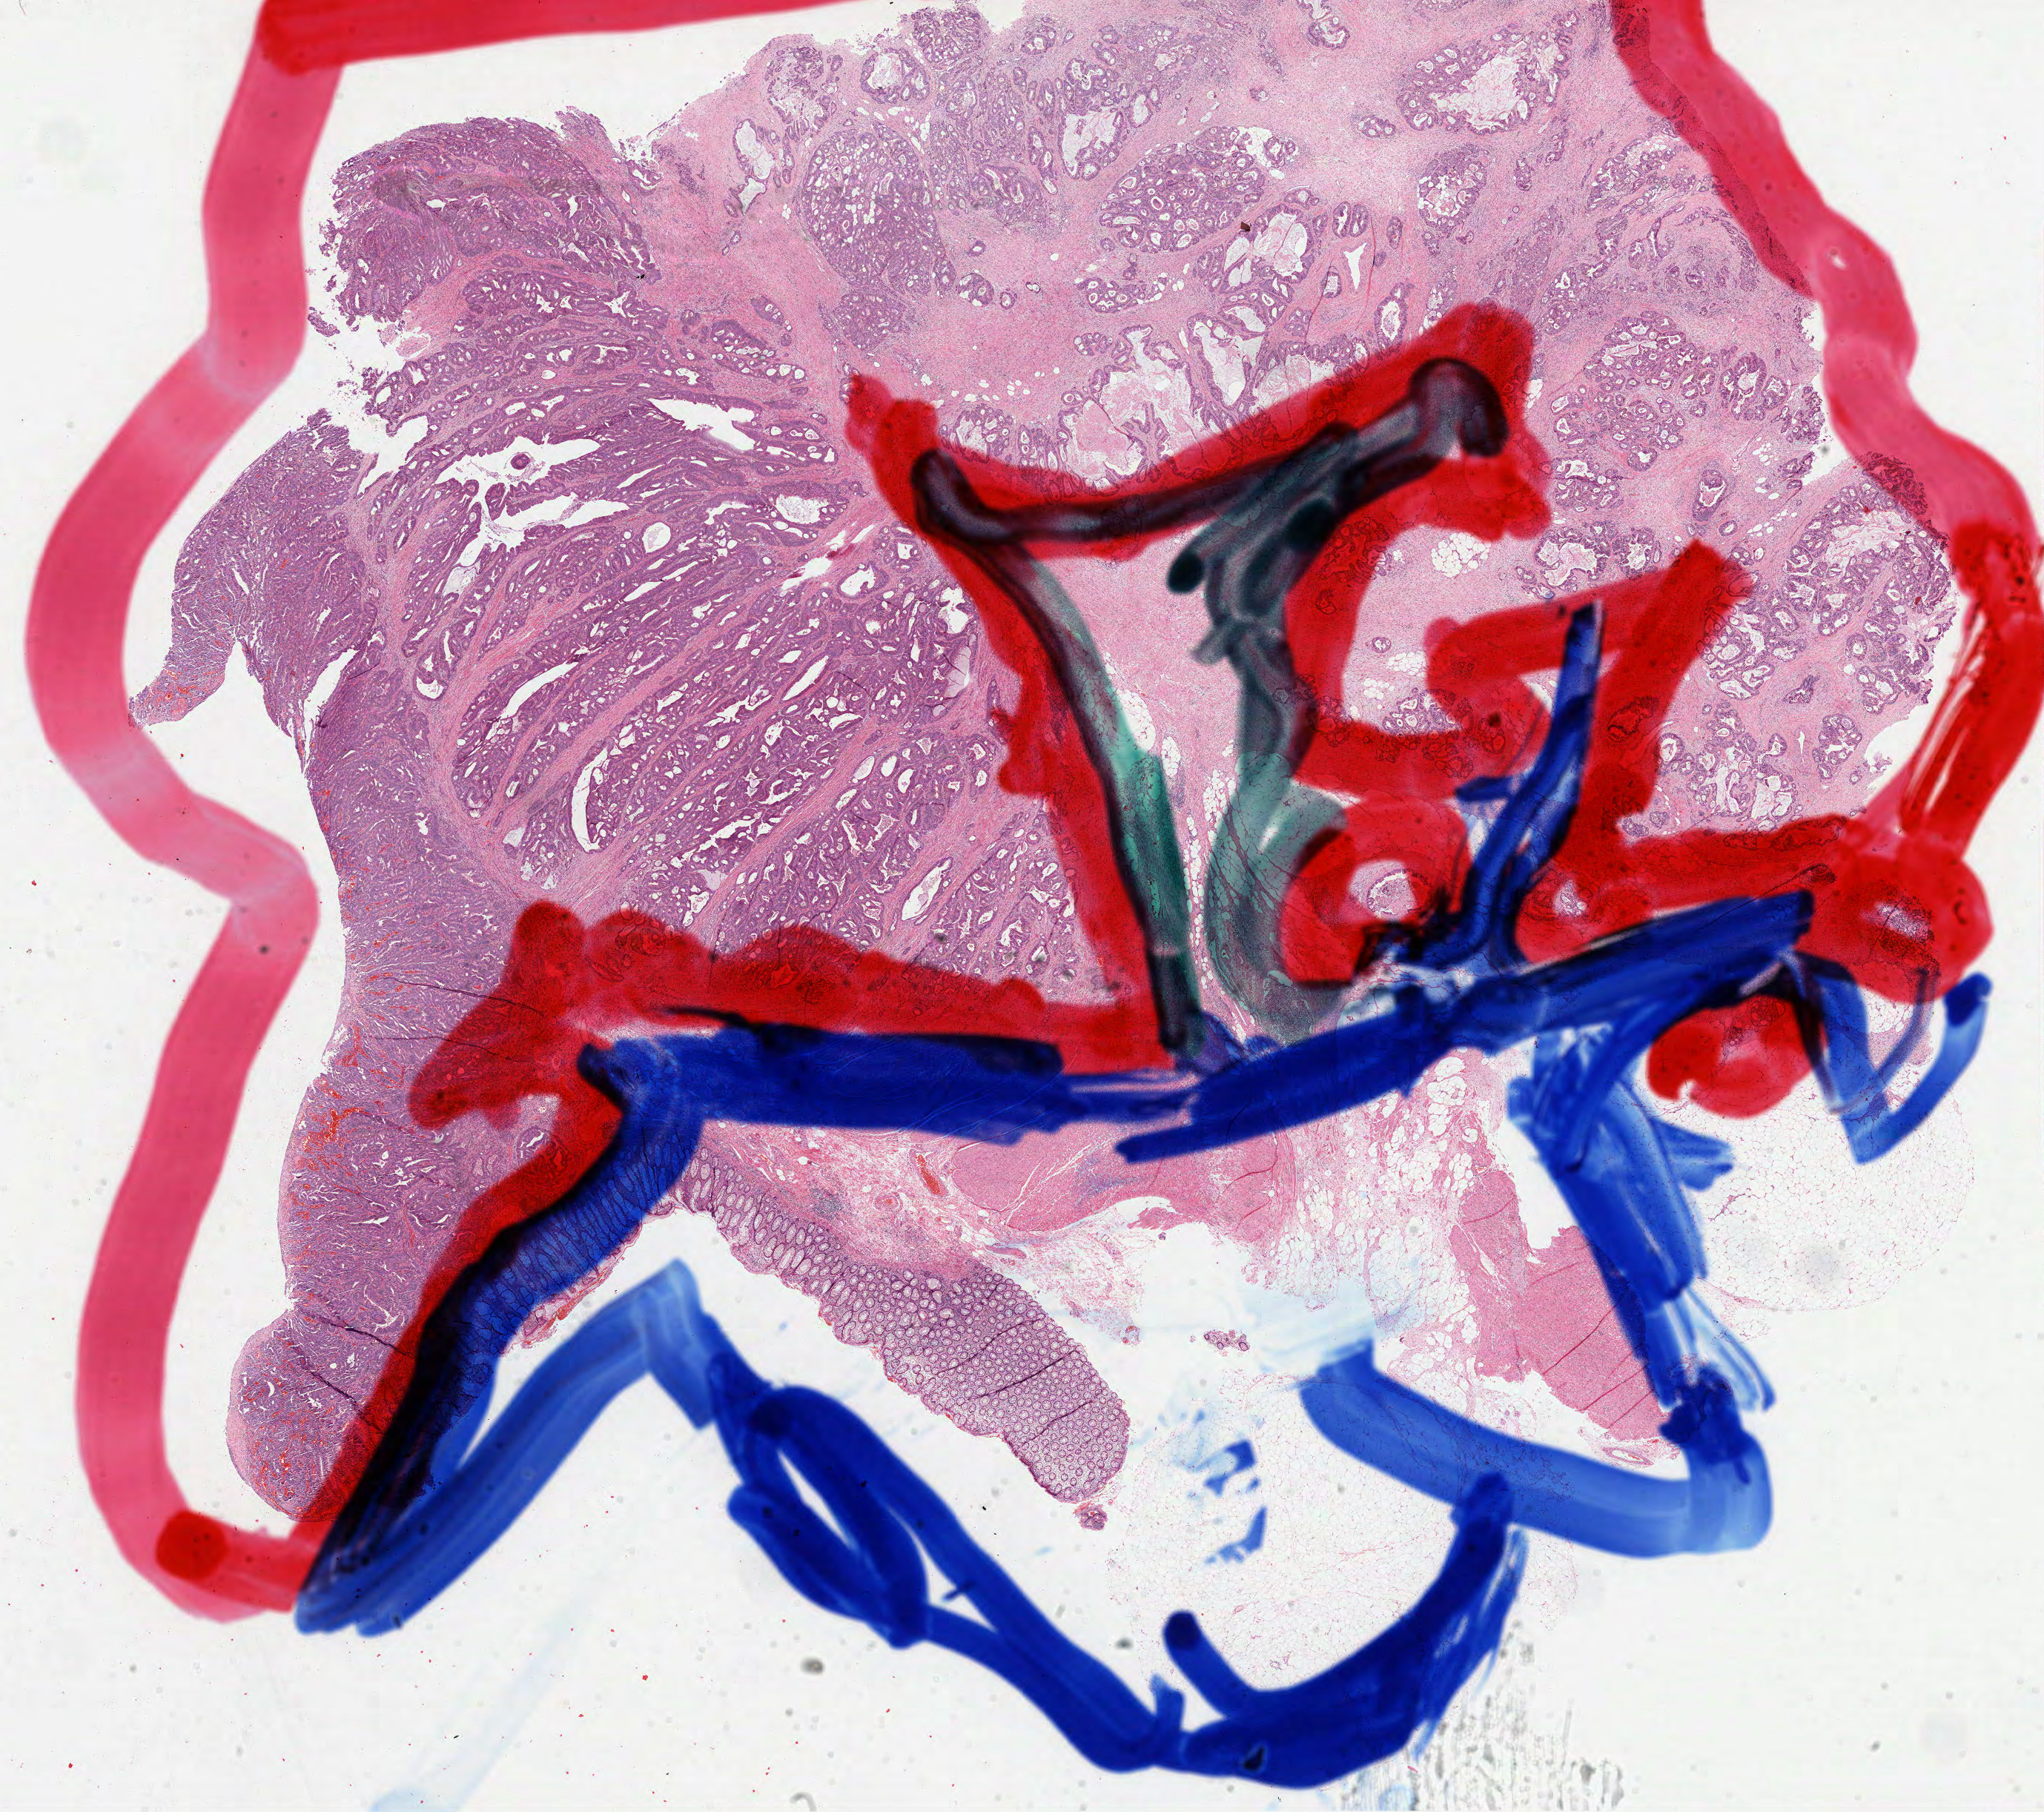
Whole-slide histology image, H&E, a low-resolution overview of the entire scanned area, about 22.2 x 19.7 mm, FFPE section, colon, primary tumour sample. Patient: female, age at initial diagnosis 52 years.
• AJCC pathologic stage: IVA (7th edition)
• diagnosis: Adenocarcinoma, NOS